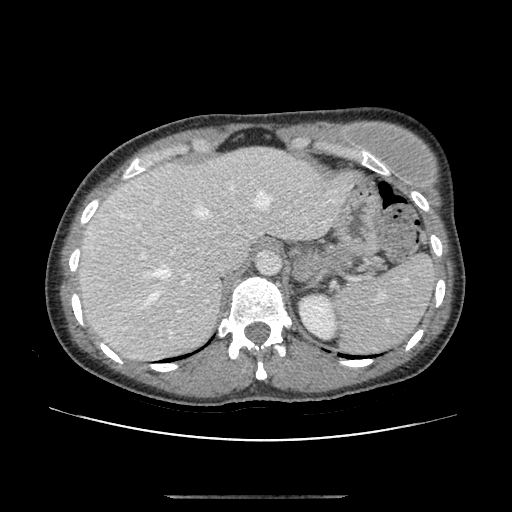
Contrast-enhanced abdominal CT, one axial slice. Slice 80 of 179 in the series (ordered by position). Reconstruction kernel STANDARD. Soft-tissue window (W 400 / L 40 HU). 2.5 mm slice thickness. 512 × 512 image matrix, field of view 360 × 360 mm. Female patient, age 51 years. Case-level facts recorded for this patient, not image findings: diagnosis: adrenocortical carcinoma; tumour side: left adrenal; tumour size at pathology: 3.5 cm; Ki-67 index: 45 %; stage (as recorded): 1.
Outlined on this slice (semi-automatic segmentation, software-assisted and operator-edited):
- mass: bounding box <294,252,318,280> (left, top, right, bottom; pixels)